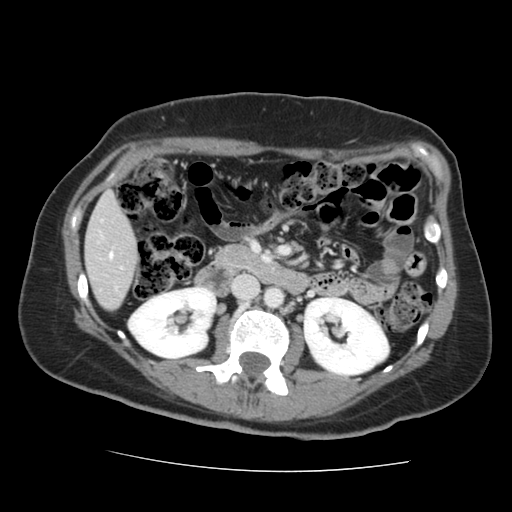
Contrast-enhanced abdominal CT, one axial slice; position 57 of 144 along the scan axis; 120 kVp; intravenous contrast given; soft-tissue window (W 400 / L 40 HU); 512 × 512 image matrix, field of view 333 × 333 mm. Female patient, age 46 years. Case-level facts recorded for this patient, not image findings: diagnosis: colorectal cancer liver metastases, imaged before liver resection.
Structures marked on this image (manually delineated by an expert):
- liver: bounding box [x1, y1, x2, y2] px = [86, 195, 136, 309]
- planned liver remnant (the part of the liver to remain after resection): [86, 195, 136, 271]
- portal vein (with intrahepatic branches): [109, 253, 113, 259]